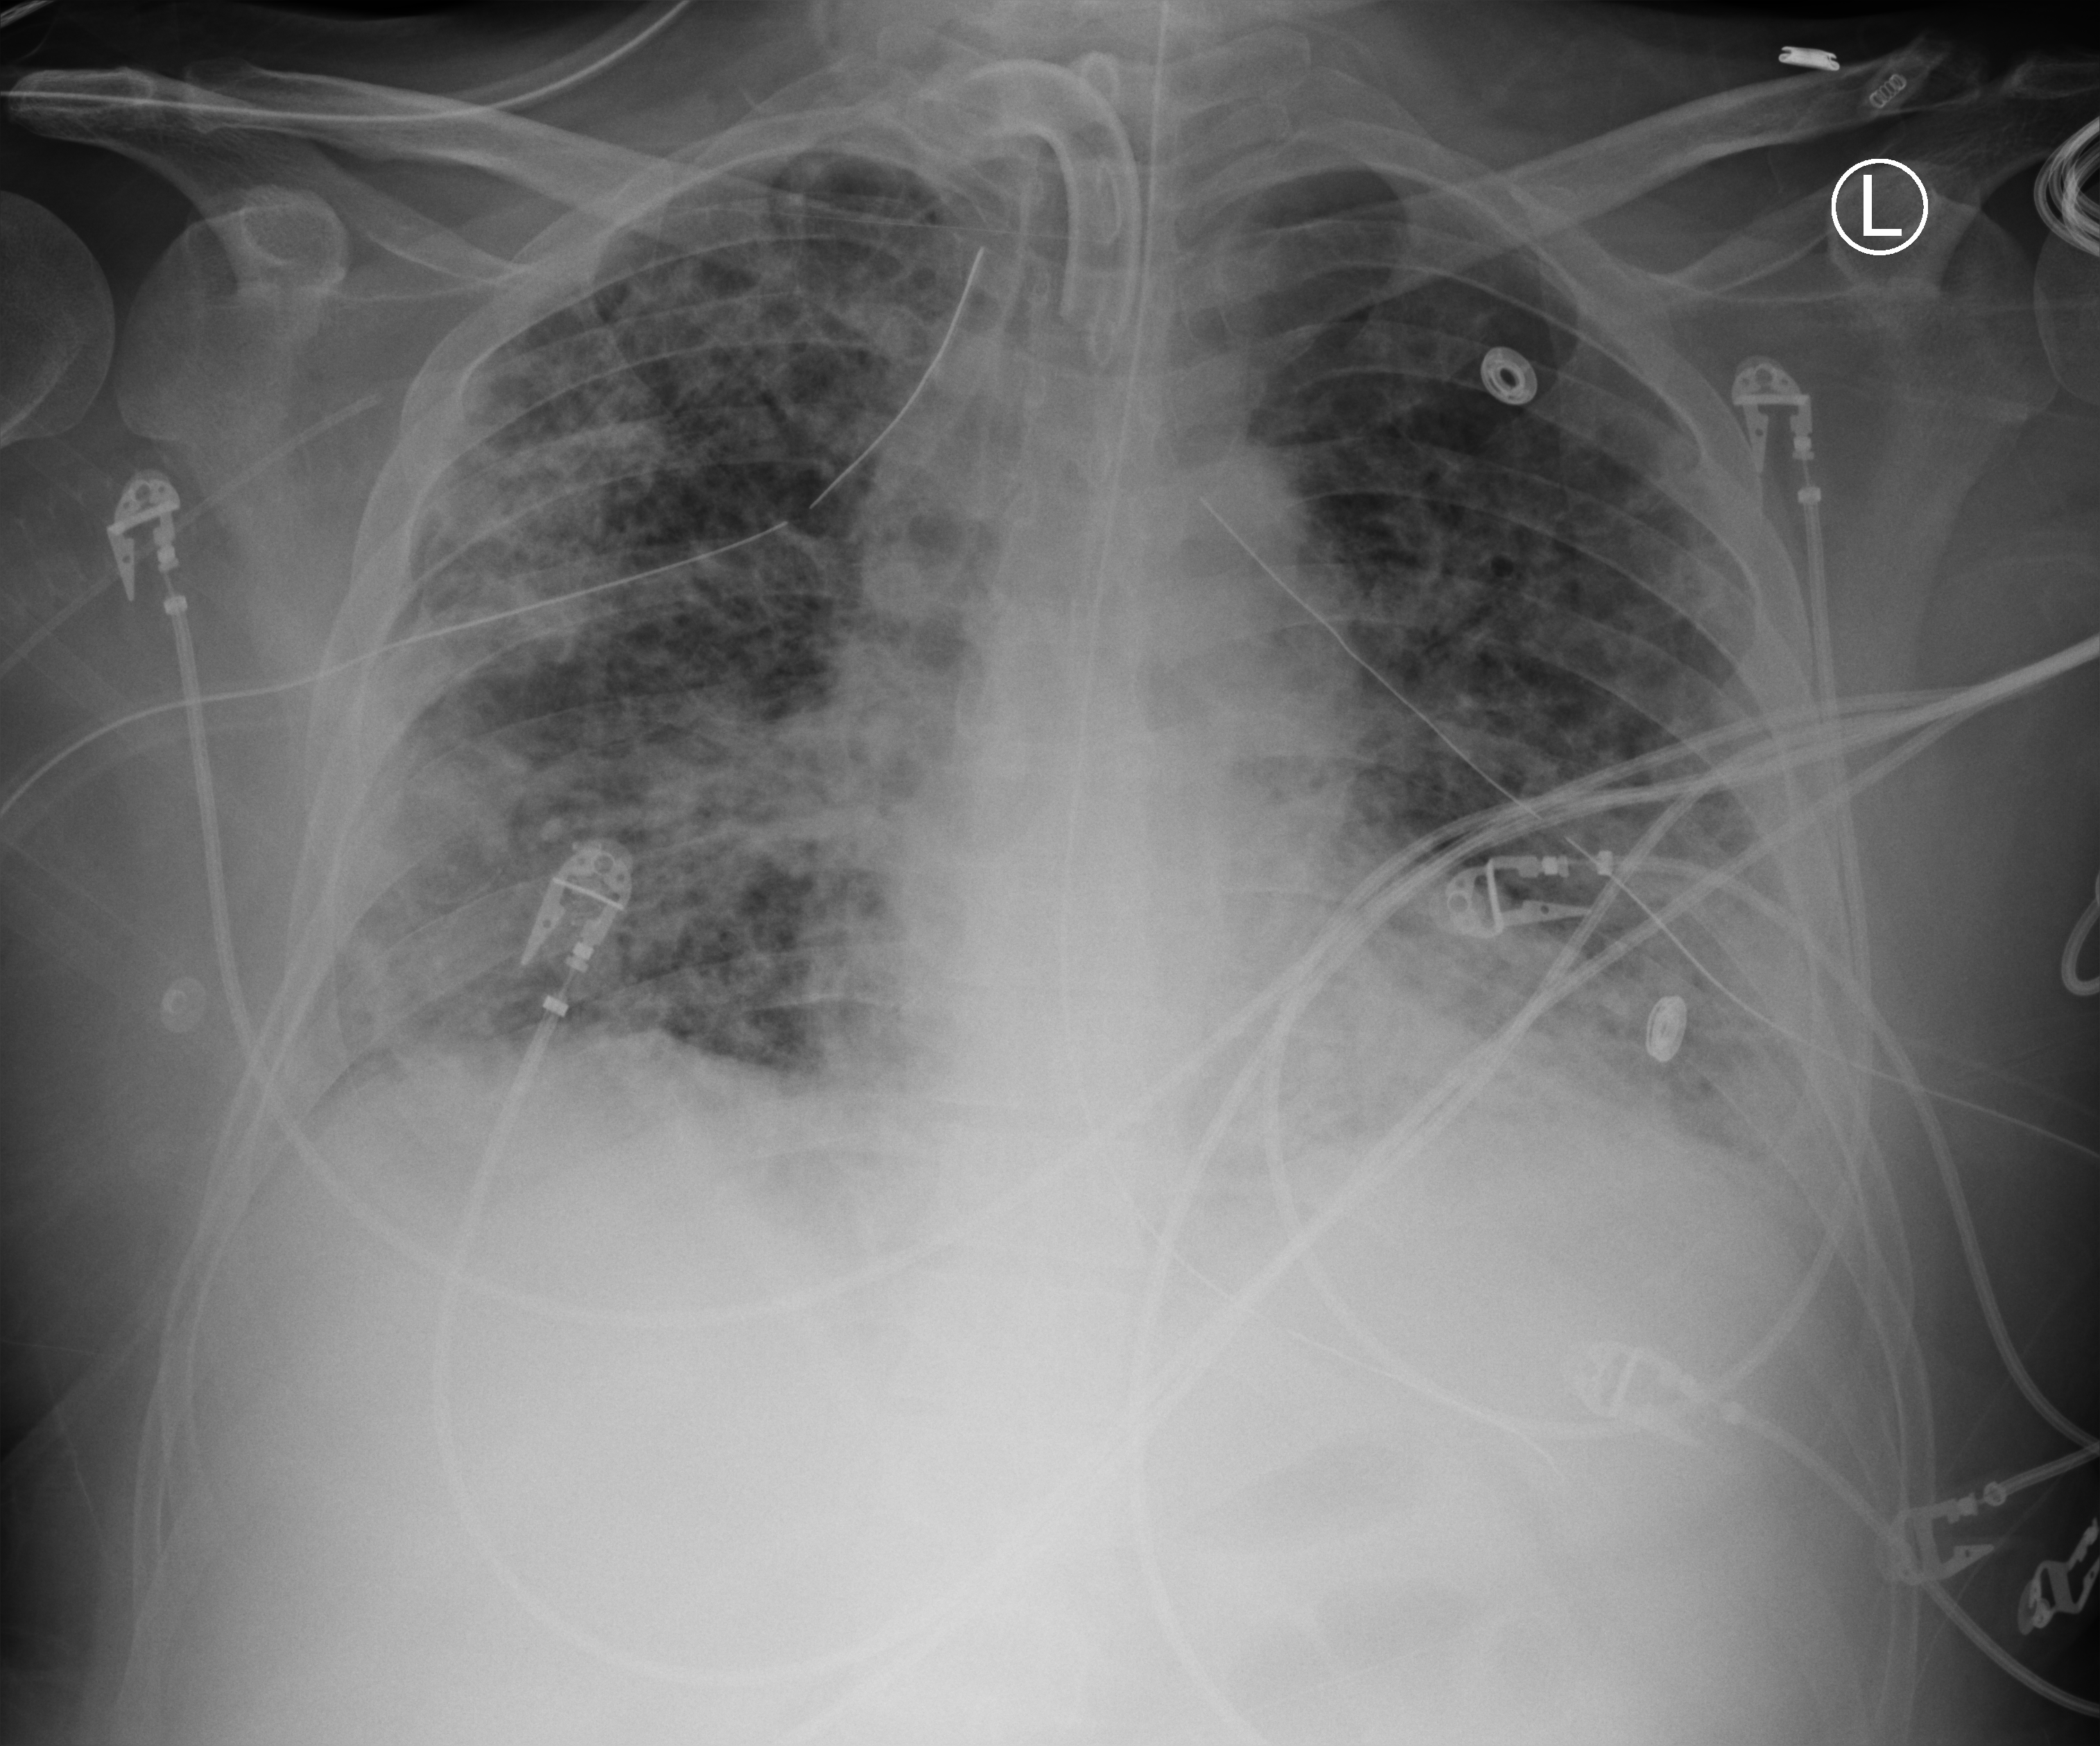
Portable chest radiograph; anteroposterior (AP) projection. Patient hospitalised with COVID-19; male, aged 18–59 years.
Hospital-stay facts (about this admission, not read from this image; timing relative to this image not recorded):
- admitted to intensive care during this hospital stay: yes
- length of hospital stay: 63 days
- mechanically ventilated during this hospital stay: yes